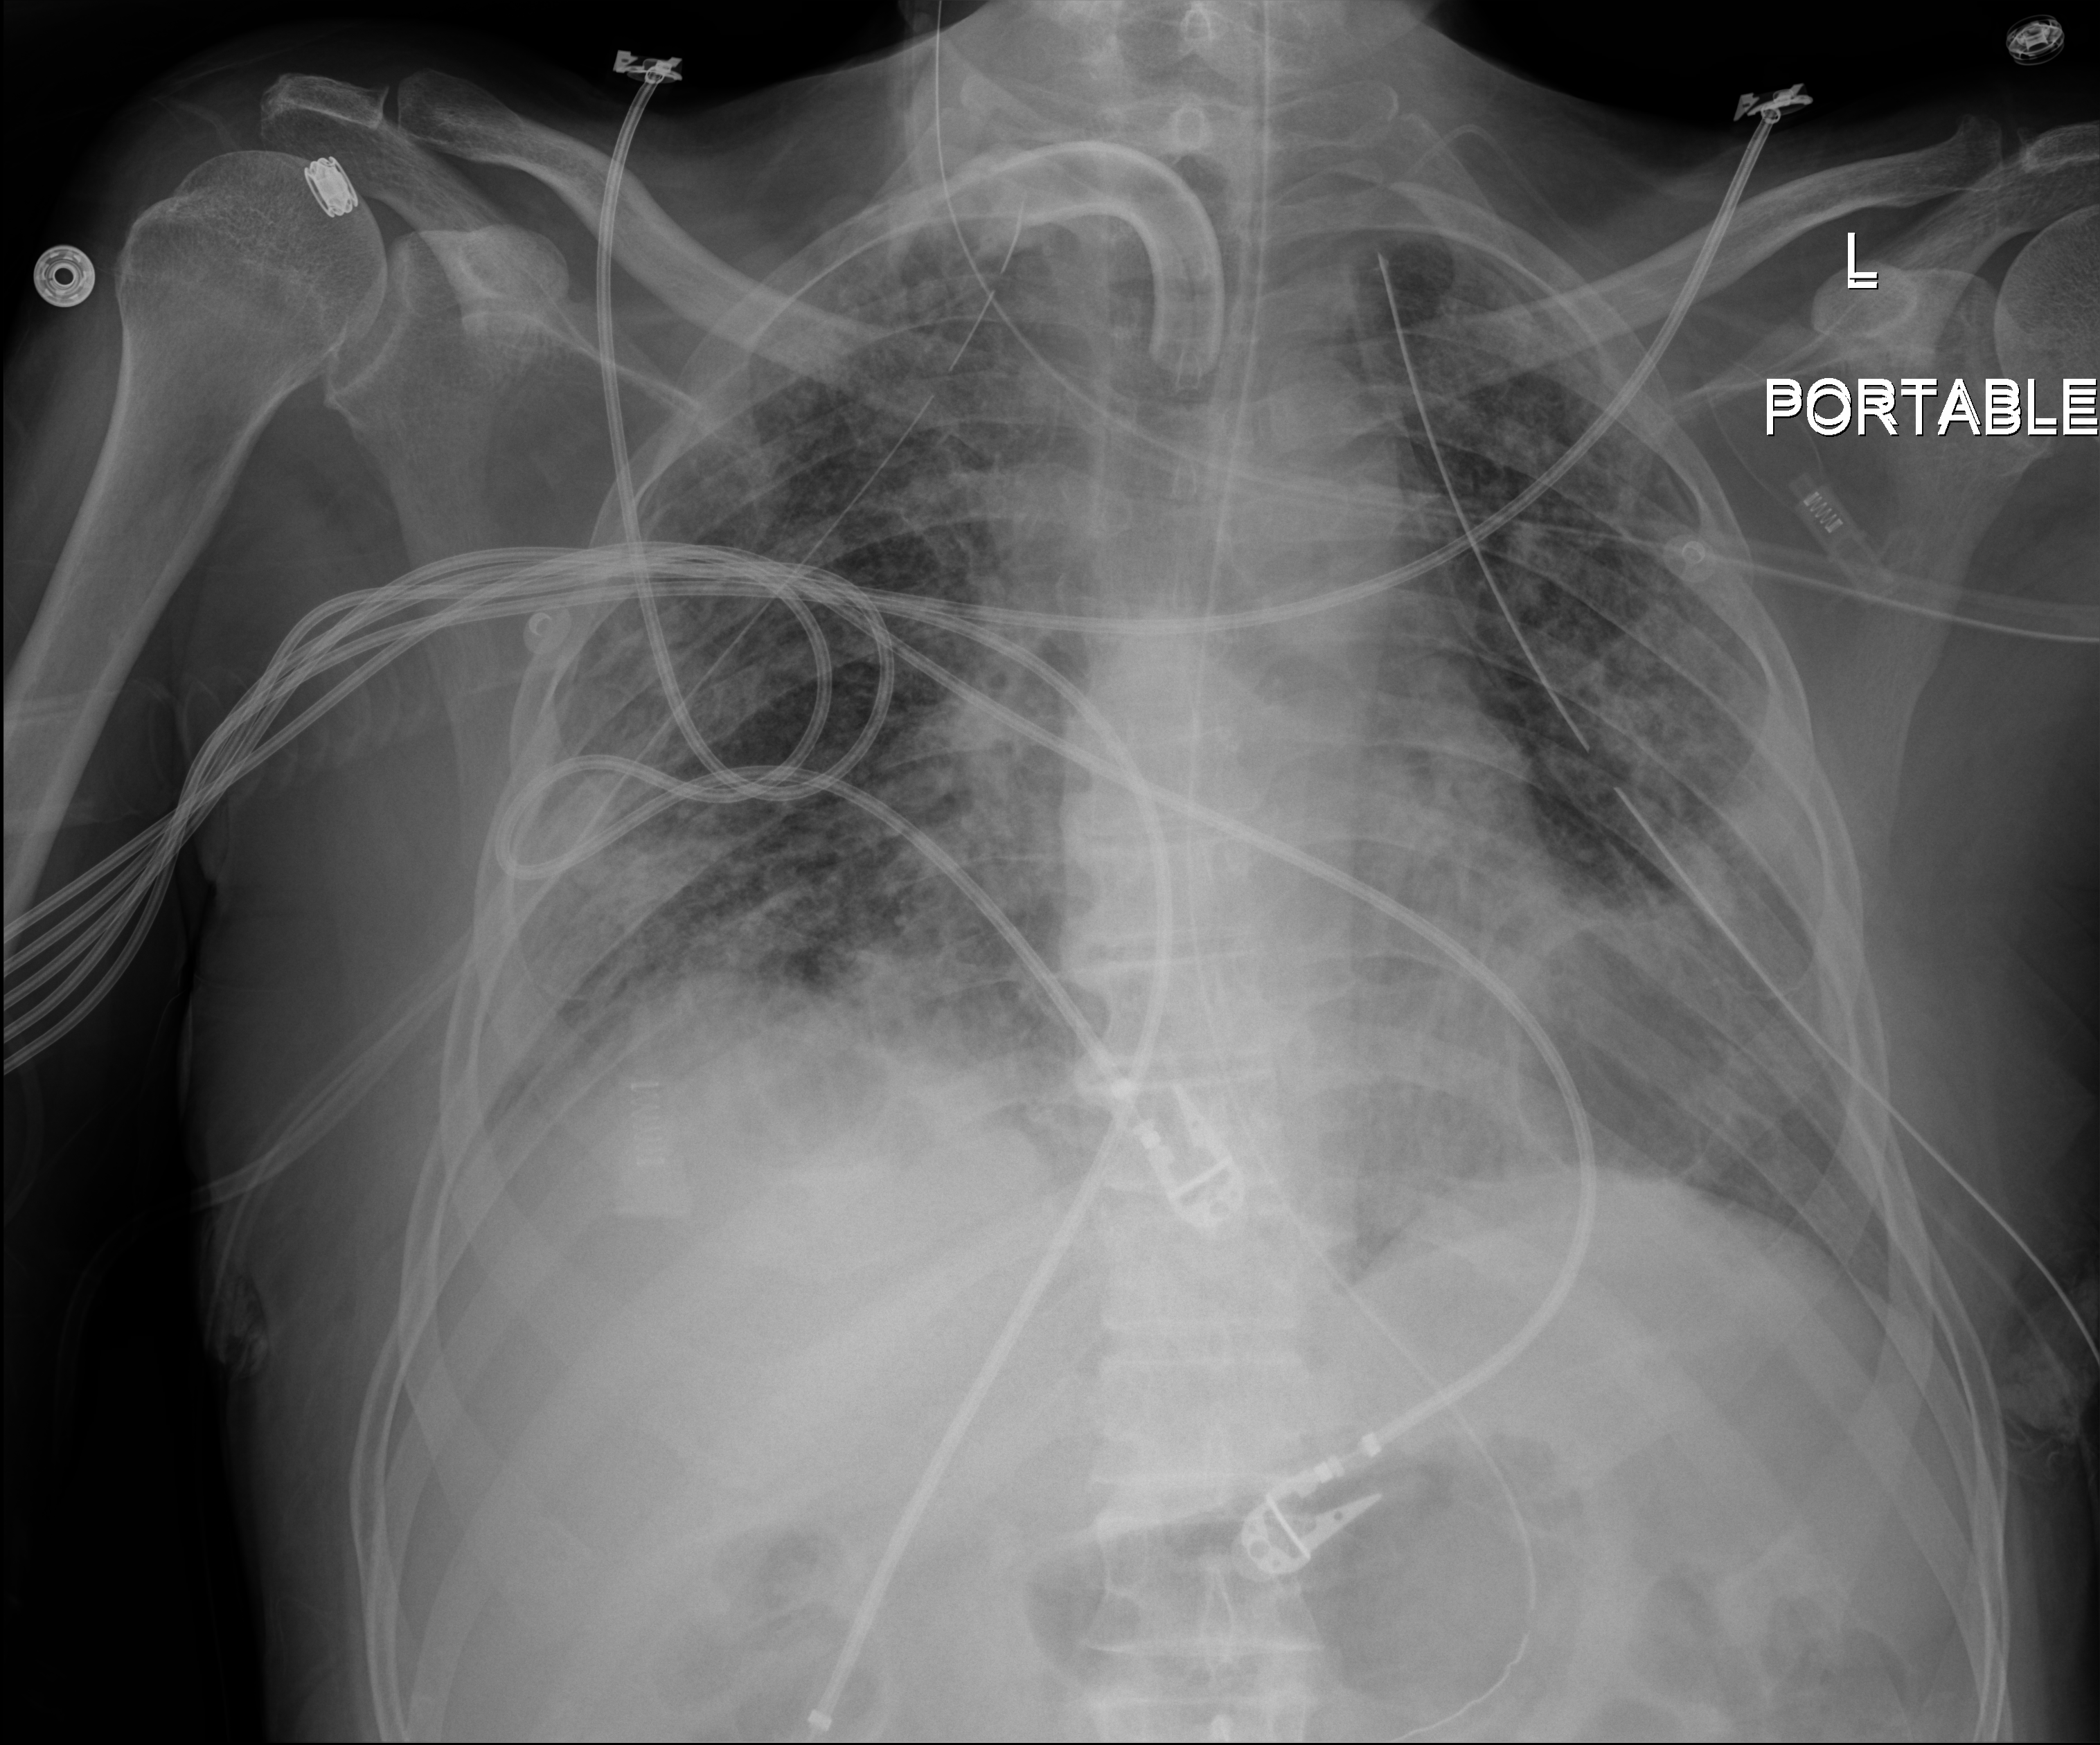
Portable chest radiograph, anteroposterior (AP) projection. Patient hospitalised with COVID-19; male, aged 18–59 years.
From the hospital-stay record, not from the radiograph (when in the stay this image was taken is not recorded):
- mechanically ventilated during this hospital stay: yes
- admitted to intensive care during this hospital stay: yes